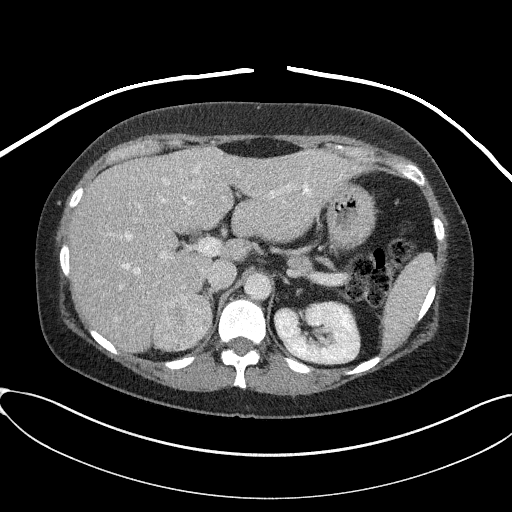
Contrast-enhanced abdominal CT, one axial slice; slice 57 of 95 in the series (ordered by position); reconstruction kernel I41f/2; intravenous contrast given; soft-tissue window (W 400 / L 40 HU); 512 × 512 image matrix, field of view 410 × 410 mm. Patient: female, 46 years. Case-level facts recorded for this patient, not image findings: diagnosis: adrenocortical carcinoma; tumour side: right adrenal; tumour size at pathology: 7.2 cm; Ki-67 index: 50 %; stage (as recorded): 4.
Outlined on this slice (semi-automatic segmentation, software-assisted and operator-edited):
- mass: bounding box [x1, y1, x2, y2] px = [154, 294, 211, 349]